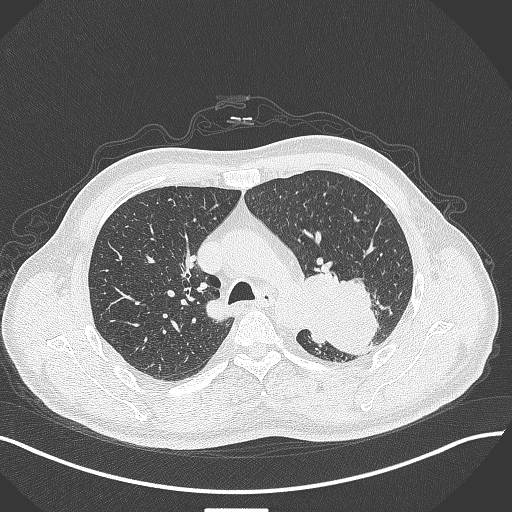
Chest CT, one axial slice. Slice 297 of 429 in the series (ordered by position). Lung window (W 1500 / L -600 HU). 1 mm slice thickness. 512 × 512 image matrix, field of view 400 × 400 mm. Male patient, age 55 years. Case-level facts recorded for this patient, not image findings: clinical TNM (as recorded): T3 N0 M1c.
Annotated regions visible in this slice (rectangle marked by the reading radiologist):
- lung tumour (recorded histology: adenocarcinoma): bounding box (x1, y1, x2, y2) in pixels: (303, 267, 380, 357)